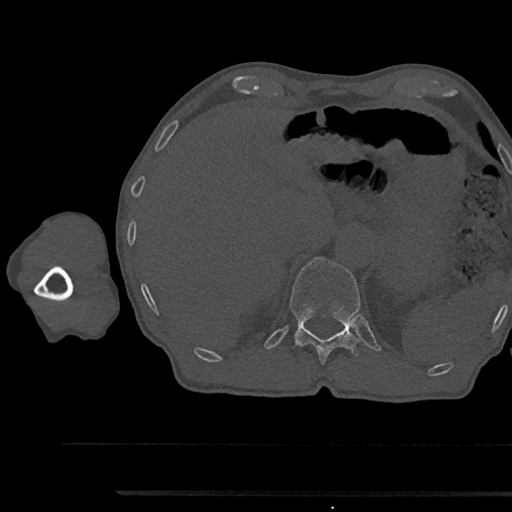
CT including the spine, one axial slice; slice 713 of 797 in the series (ordered by position); reconstruction kernel Br40s/3; bone window (W 1800 / L 400 HU); 0.5 mm slice thickness; 512 × 512 image matrix, field of view 367 × 367 mm. Male patient, age 79 years. From the clinical record (not read from this slice): primary cancer: prostate.
Outlined on this slice (semi-automatic segmentation, software-assisted and operator-edited):
- T12 vertebra: bounding box [x1, y1, x2, y2] px = [290, 257, 361, 365]